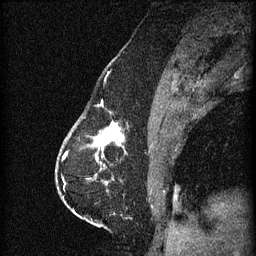
Breast MRI (dynamic contrast-enhanced), one sagittal slice; position 24 of 60 along the scan axis; 3 images stored at this slice position (order not interpretable as contrast timing); 1.5 T; TE 4.2 ms, TR 11 ms; 256 × 256 image matrix, field of view 180 × 180 mm. Patient: female, 63 years.
Structures marked on this image (semi-automatic segmentation, software-assisted and operator-edited):
- analysis volume of interest (the breast-tissue region the enhancement analysis was run in; not a lesion): box from (x=86, y=122) to (x=129, y=153) px
- tumour enhancement mask (voxels above the 70 % enhancement threshold inside the analysis volume of interest): (x=94, y=122)–(x=125, y=151)